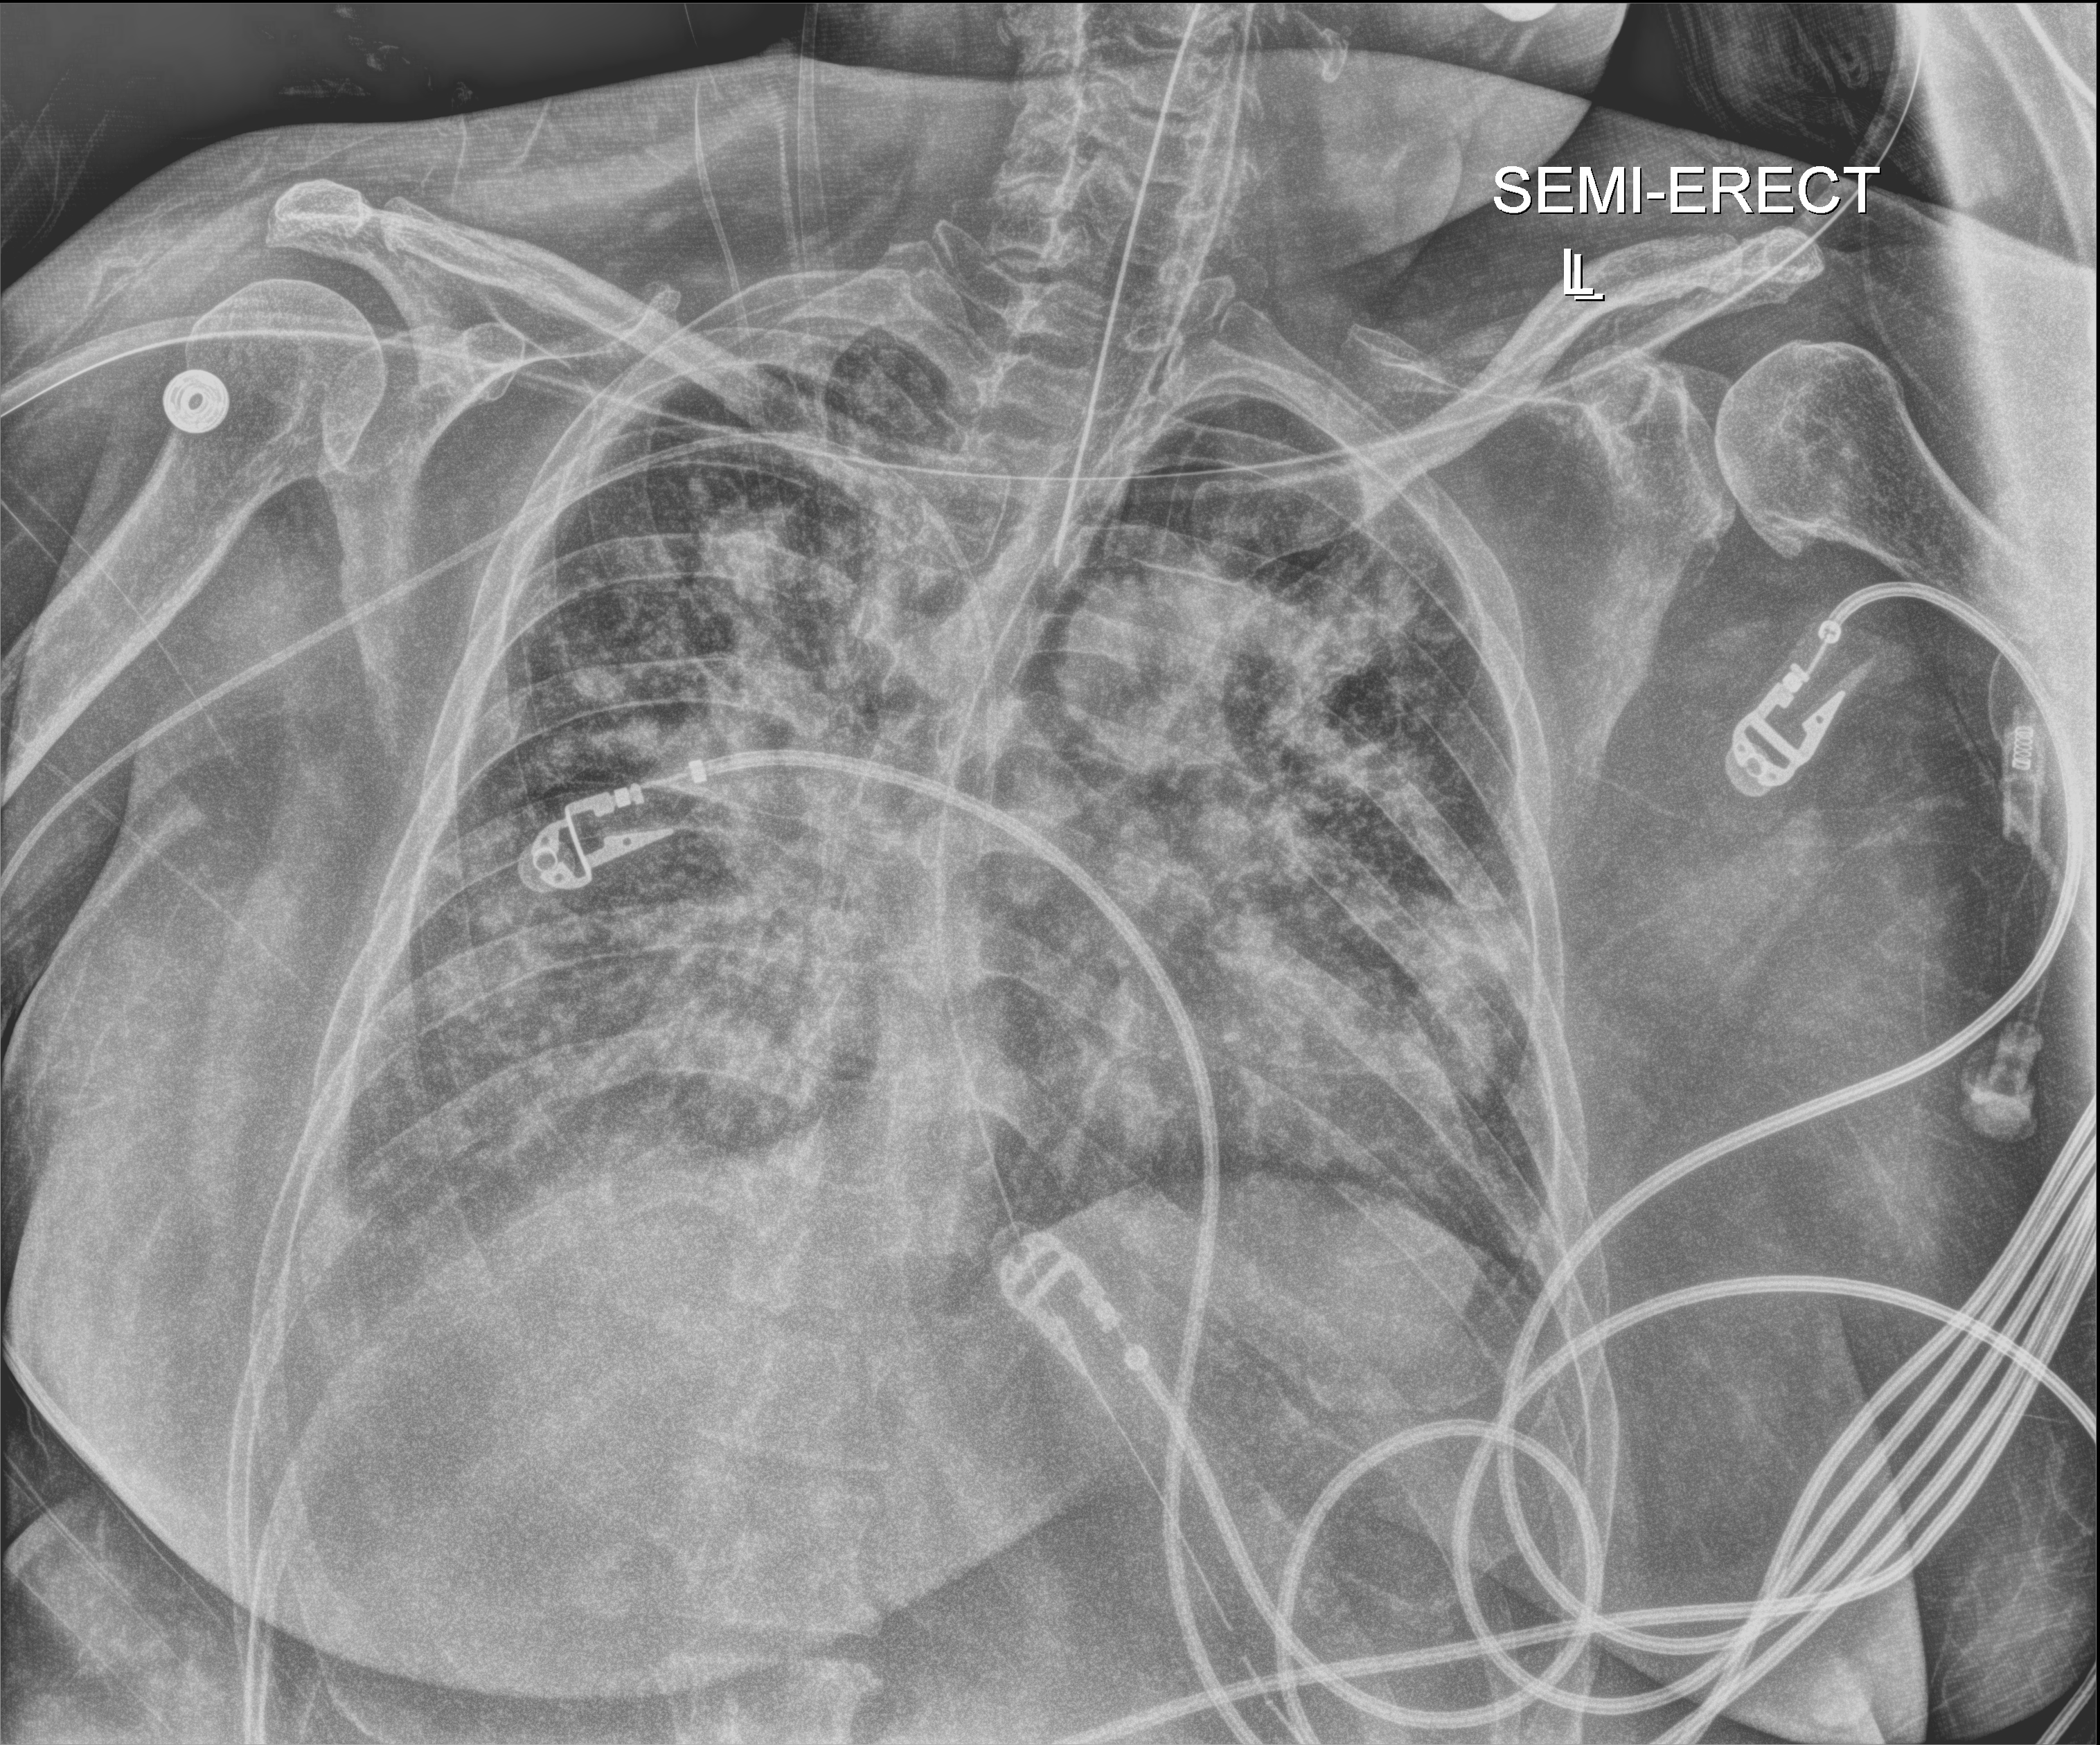
Portable chest radiograph; anteroposterior (AP) projection. Patient hospitalised with COVID-19, aged 18–59 years.
Admission-level facts for this patient (not findings on this image; timing relative to this image not recorded):
- admitted to intensive care during this hospital stay: yes
- mechanically ventilated during this hospital stay: yes